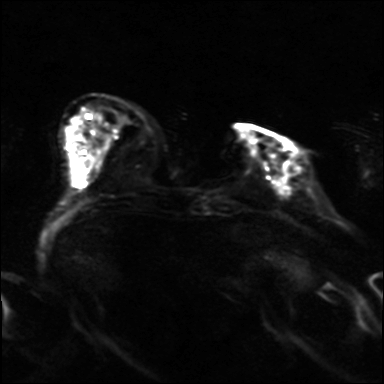
Breast MRI, one axial slice; slice 7 of 36 in the series (ordered by position); diffusion-weighted series; image 2 of 4 stored at this slice position (different b-values; order by instance number); 3 T; 4 mm slice thickness; 384 × 384 image matrix, field of view 320 × 320 mm. Female patient.
Structures marked on this image (outlined manually by an expert reader):
- tumour on diffusion-weighted imaging: bounding box <285,167,291,185> (left, top, right, bottom; pixels)